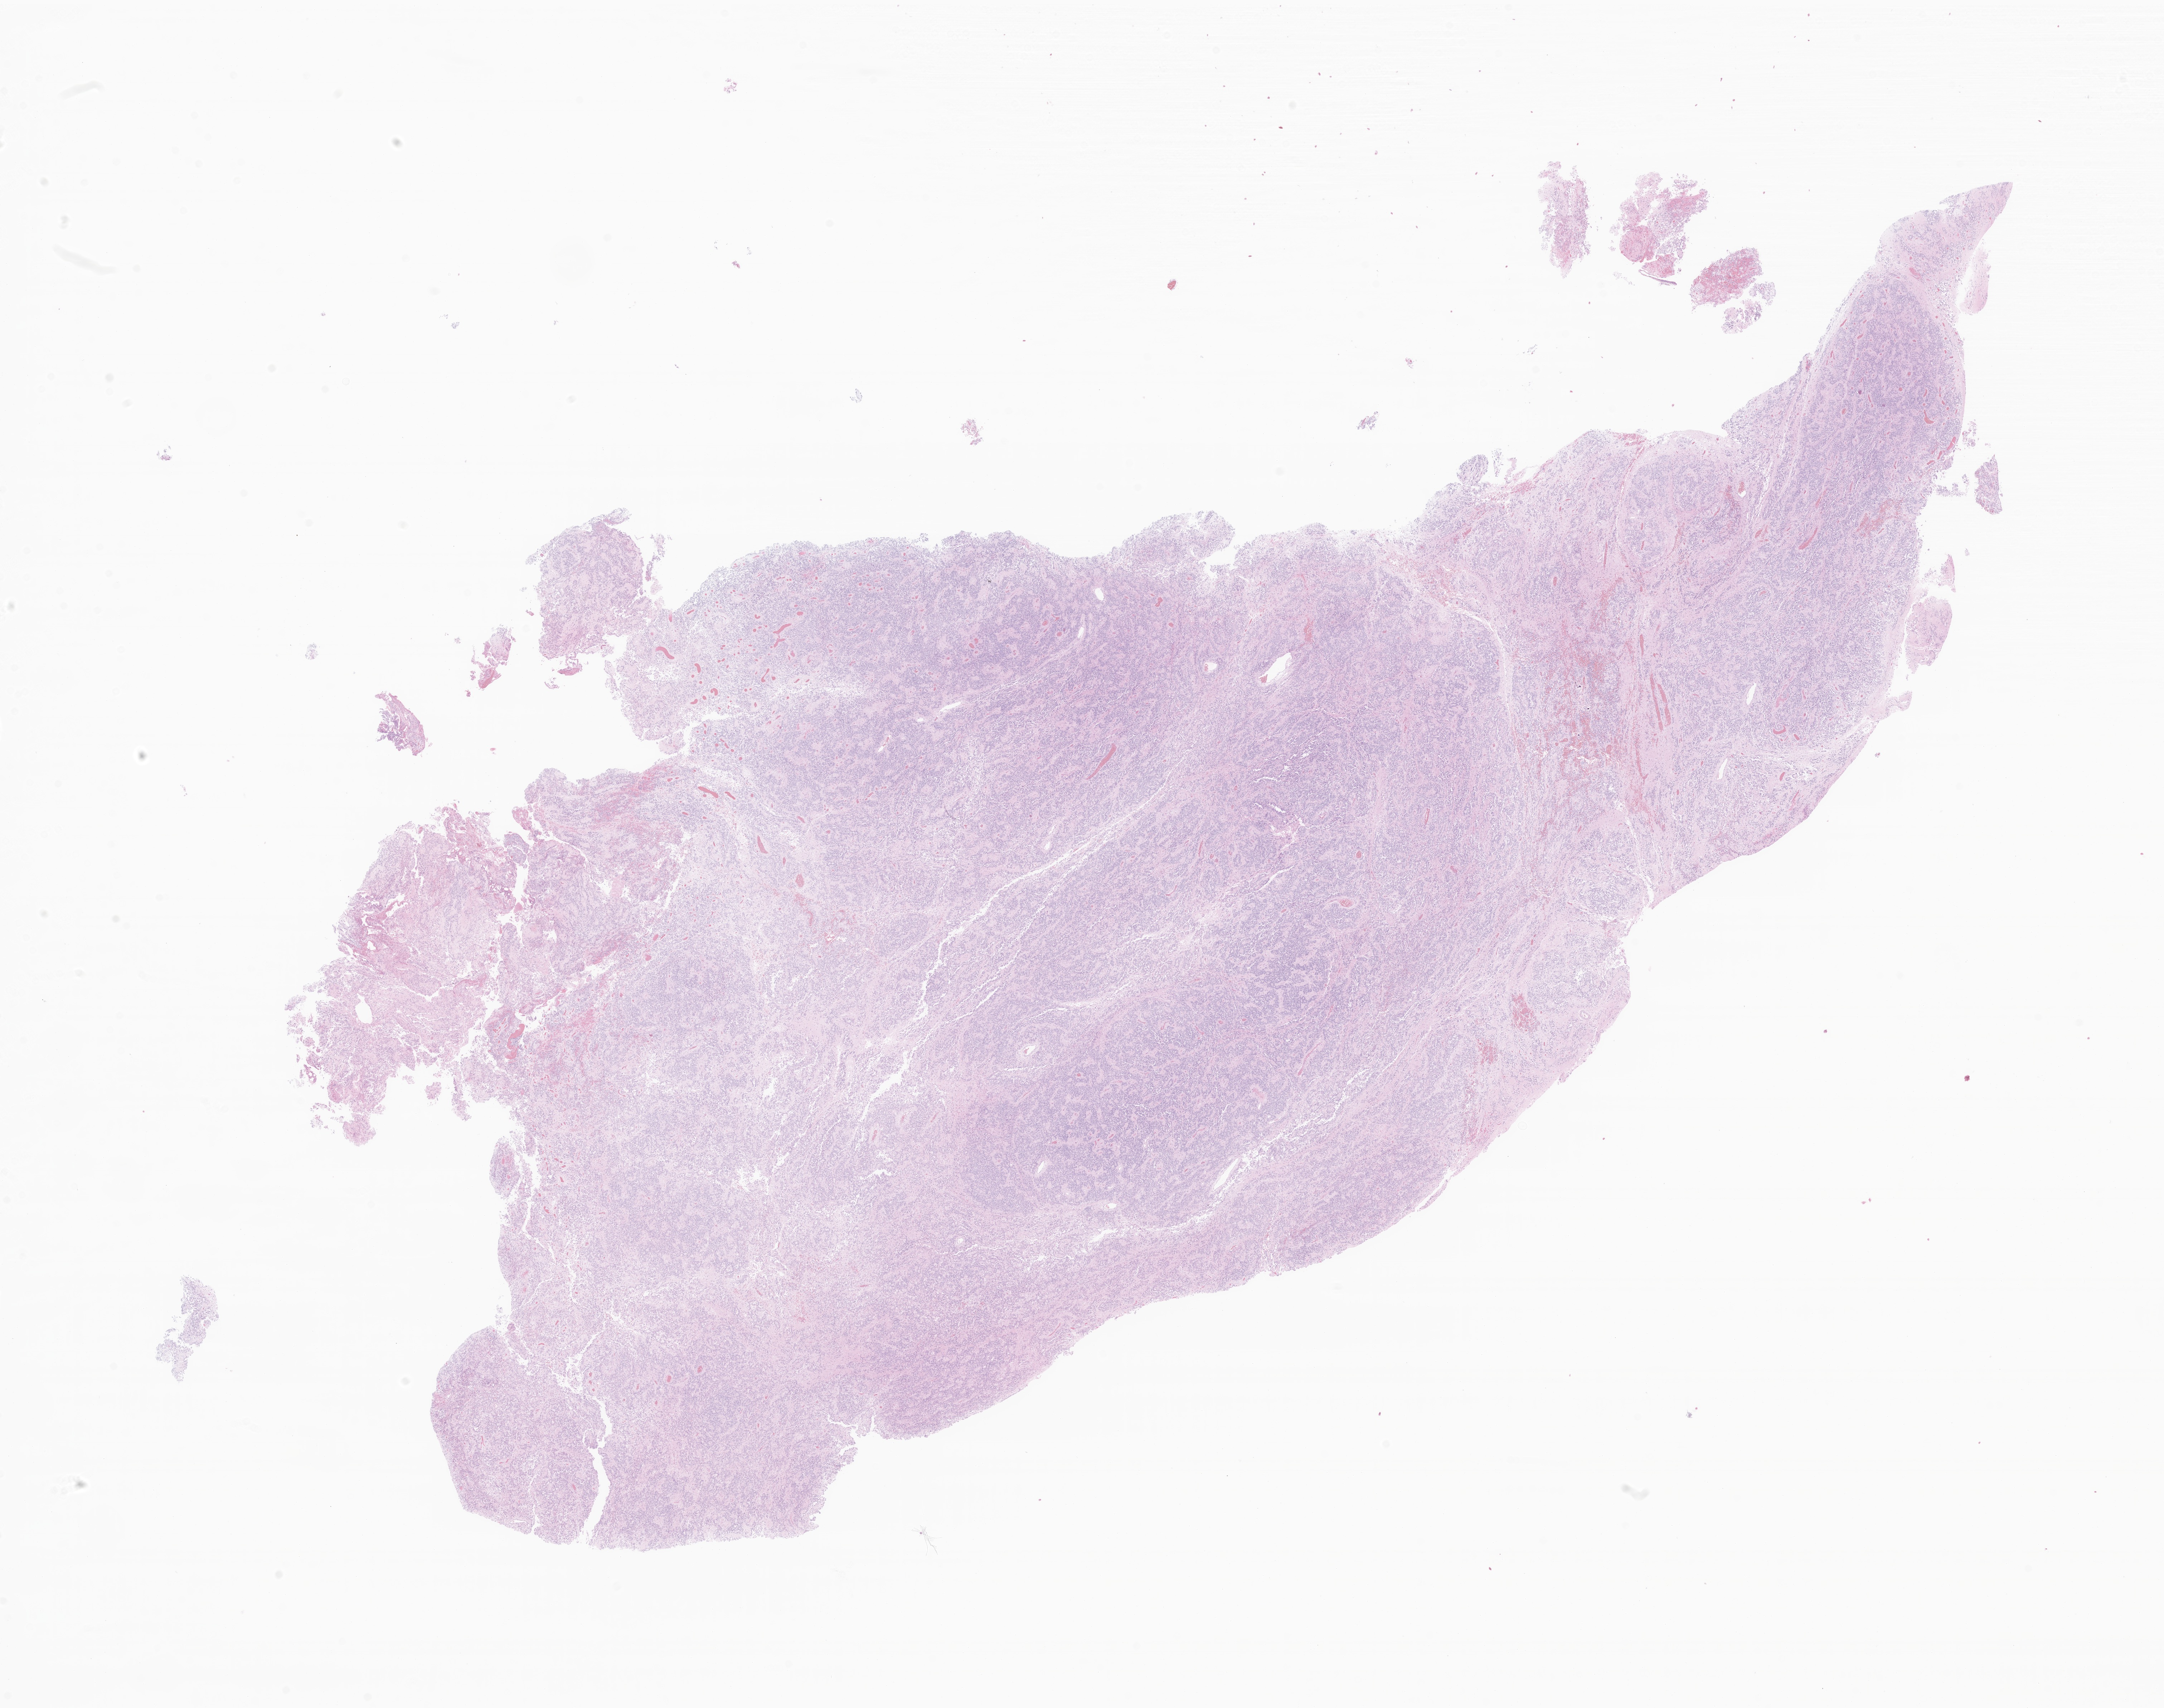
Whole-slide image, H&E stain of tumor tissue from the cerebral ventricle, shown as a low-resolution overview of the whole scanned area (about 25.5 x 20.1 mm). Formalin-fixed paraffin-embedded section. Male patient, age 45 months (3 years 9 months).
Diagnosis: Ependymoma, NOS.